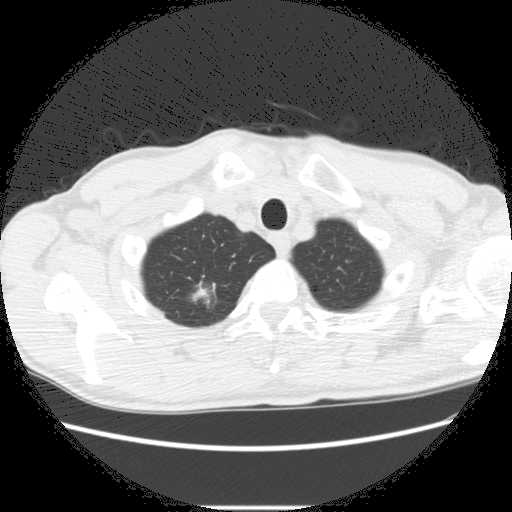
Axial slice from a low-dose chest CT screening exam; second screening round (one year after baseline); lung window (W 1500 / L -600 HU); standard (soft-tissue) reconstruction kernel (STANDARD). Male participant, aged 66 years at enrolment. Former smoker at enrolment.
Lesion marked by an expert reader, bounding box (x1, y1, x2, y2) in pixels: (172, 278, 232, 326). The screening reader recorded 5 non-calcified nodules or masses ≥4 mm on this exam (right lower lobe, right upper lobe, right upper lobe, right upper lobe, left lower lobe); which of them this box marks is not recorded. Participant outcome: lung cancer diagnosed 75 days after this screen — adenocarcinoma, NOS, right upper lobe, undifferentiated (G4), stage IA (AJCC 6th edition), 20 mm at pathology.